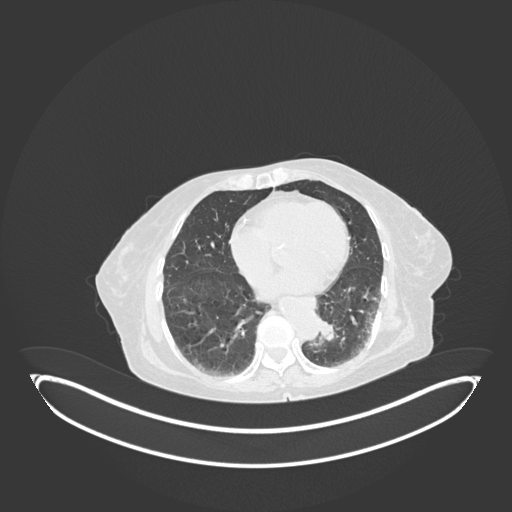
Chest CT, one axial slice. Position 29 of 189 along the scan axis. 120 kVp. Lung window (W 1500 / L -600 HU). 1 mm slice thickness. 512 × 512 image matrix. Female patient, age 82 years. Case-level facts recorded for this patient, not image findings: clinical TNM (as recorded): T1b N0 M1.
Annotated regions visible in this slice (rectangle marked by the reading radiologist):
- lung tumour (recorded histology: adenocarcinoma): bounding box [x1, y1, x2, y2] px = [313, 312, 340, 346]